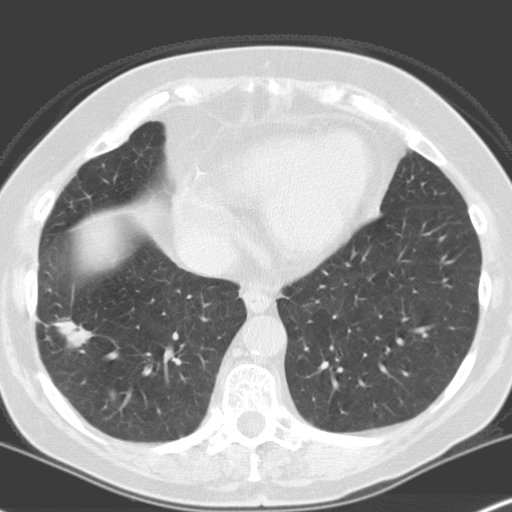
Low-dose screening chest CT, axial slice. First (baseline) screen. Lung window (W 1500 / L -600 HU). 3.2 mm slice thickness. Slice 100 of 160 in the series. Female participant, aged 70 years at enrolment.
• Lesion marked by an expert reader, bounding box (x1, y1, x2, y2) in pixels: (30, 295, 100, 363).
• The screening reader recorded 4 non-calcified nodules or masses ≥4 mm on this exam (right lower lobe, right upper lobe, left upper lobe, left upper lobe); which of them this box marks is not recorded.
• Official screen result: positive, change unspecified: nodule(s) >= 4 mm or enlarging nodule(s), mass(es), or other non-specific abnormalities suspicious for lung cancer.
• Later outcome: lung cancer diagnosed 28 days after this screen — adenocarcinoma, NOS, right lower lobe, moderately differentiated (G2), stage IV (AJCC 6th edition), 28 mm at pathology.